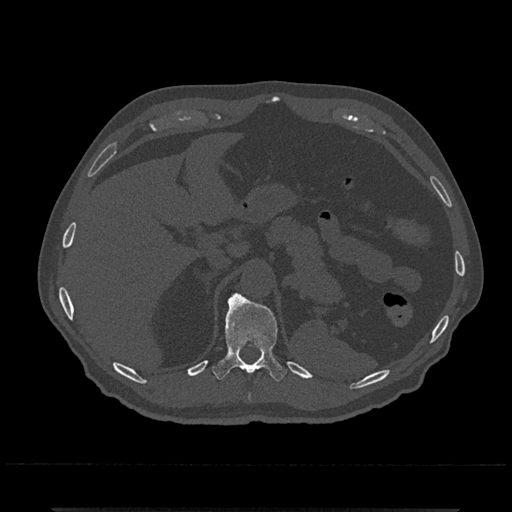
CT including the spine, one axial slice. Position 497 of 797 along the scan axis. Reconstruction kernel Br40s/3. 120 kVp. Bone window (W 1800 / L 400 HU). 0.5 mm slice thickness. 512 × 512 image matrix, field of view 393 × 393 mm. Patient: male, 67 years. Case-level facts recorded for this patient, not image findings: primary cancer: prostate.
Structures marked on this image (semi-automatically segmented with operator editing):
- T11 vertebra: bounding box [x1, y1, x2, y2] px = [212, 291, 287, 383]